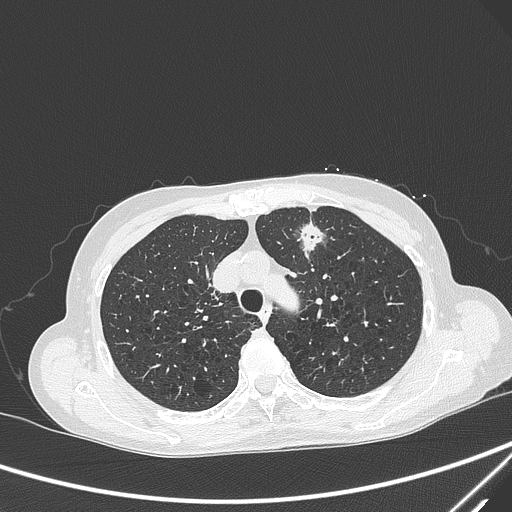
Chest CT, one axial slice; position 228 of 299 along the scan axis; 120 kVp; lung window (W 1500 / L -600 HU); 1 mm slice thickness; 512 × 512 image matrix. Patient: female, 71 years. Case-level facts recorded for this patient, not image findings: clinical TNM (as recorded): T1c N0 M0; histopathological grade: G2-3.
Annotated regions visible in this slice (rectangle marked by the reading radiologist):
- lung tumour (recorded histology: adenocarcinoma): box from (x=295, y=221) to (x=328, y=259) px